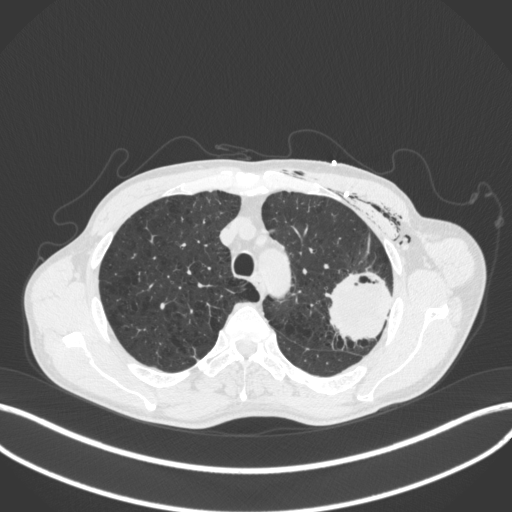
Chest CT, one axial slice. Position 311 of 416 along the scan axis. Reconstruction kernel B31f. Lung window (W 1500 / L -600 HU). 512 × 512 image matrix, field of view 400 × 400 mm. Male patient, age 58 years. Case-level facts recorded for this patient, not image findings: clinical TNM (as recorded): T3 N0 M0.
Annotated regions visible in this slice (bounding box drawn by a radiologist):
- lung tumour (recorded histology: adenocarcinoma): bounding box [x1, y1, x2, y2] px = [323, 267, 399, 347]